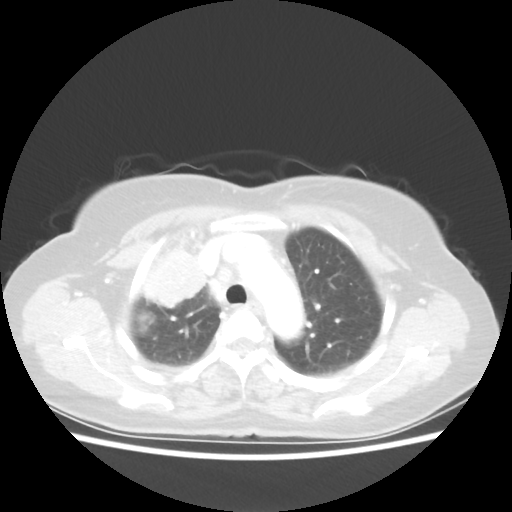
Chest CT, one axial slice; slice 41 of 55 in the series (ordered by position); reconstruction kernel STANDARD; lung window (W 1500 / L -600 HU); 5 mm slice thickness; 512 × 512 image matrix, field of view 337 × 337 mm. Patient: female, 62 years. Case-level facts recorded for this patient, not image findings: clinical TNM (as recorded): T4 N3 M0.
Outlined on this slice (bounding box drawn by a radiologist):
- lung tumour (recorded histology: squamous cell carcinoma): bounding box <143,252,215,310> (left, top, right, bottom; pixels)